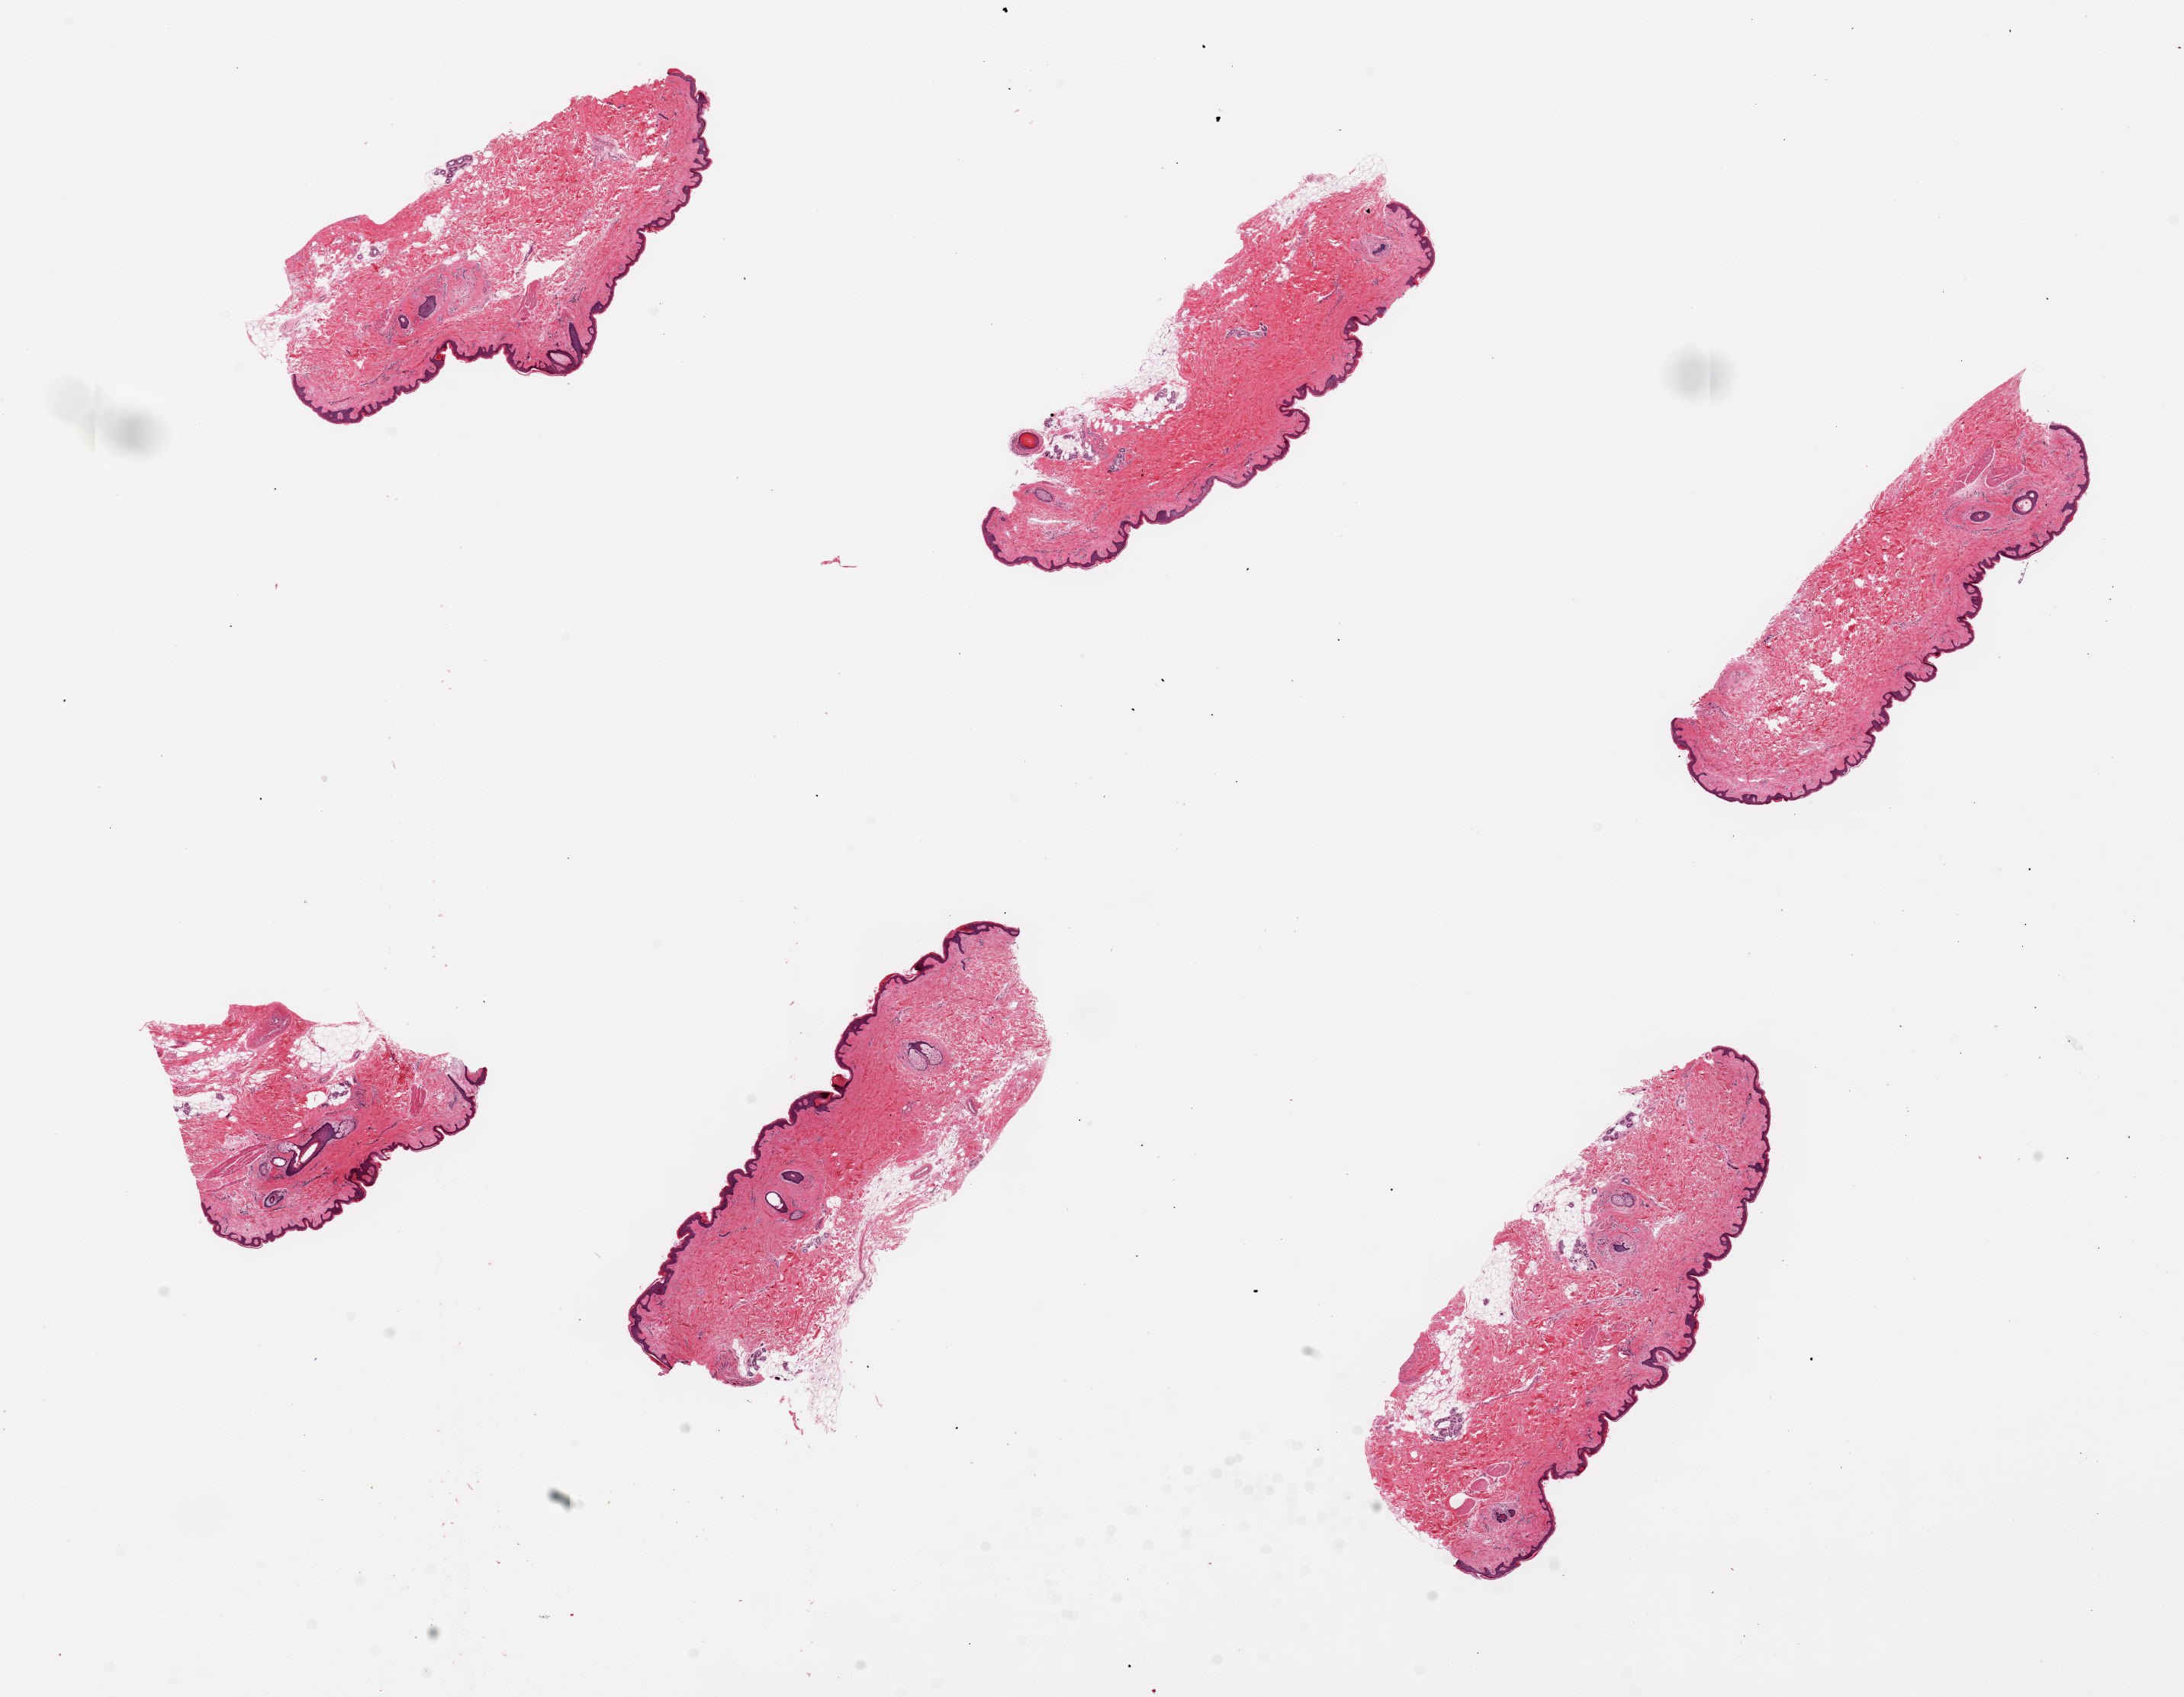
Whole-slide image, haematoxylin and eosin stain, whole scanned area (about 22.6 x 17.6 mm) shown as a low-resolution overview. PAXgene-fixed paraffin-embedded (PFPE) section. Sampled site (target tissue): skin of suprapubic region. Donor tissue sample. Donor sex: female.
Reviewer comment on this tissue sample: 6 pieces, up to 6x3mm; some focal subcutaneous adipose, otherwise well trimmed.